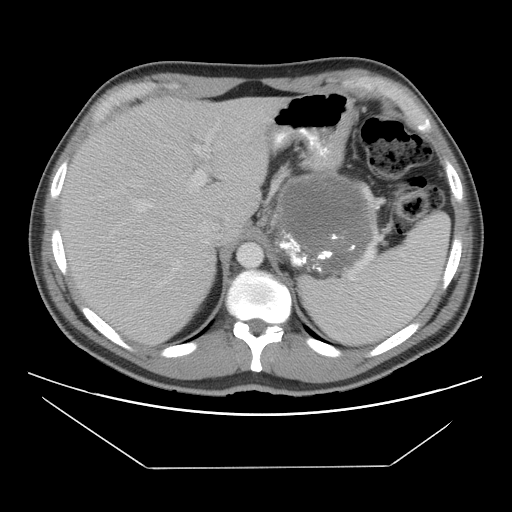
Contrast-enhanced abdominal CT, one axial slice; slice 78 of 131 in the series (ordered by position); reconstruction kernel STANDARD; 120 kVp; intravenous contrast given; soft-tissue window (W 400 / L 40 HU); 512 × 512 image matrix, field of view 396 × 396 mm. Patient: male, 44 years. Case-level facts recorded for this patient, not image findings: diagnosis: adrenocortical carcinoma; tumour side: left adrenal; tumour size at pathology: 15.5 cm; Ki-67 index: 6 %.
Structures marked on this image (semi-automatically segmented with operator editing):
- mass: box from (x=273, y=173) to (x=370, y=272) px